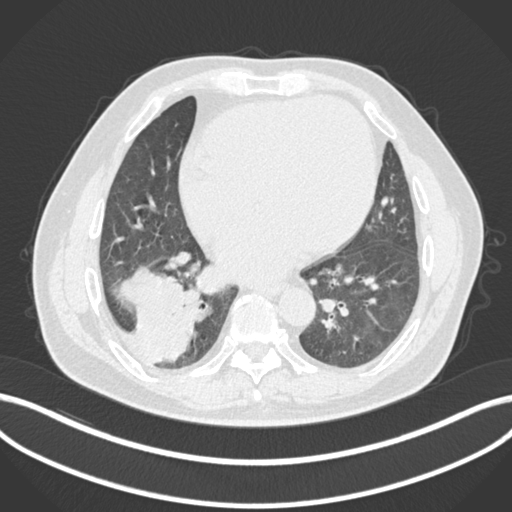
Chest CT, one axial slice. Slice 58 of 200 in the series (ordered by position). Lung window (W 1500 / L -600 HU). 512 × 512 image matrix, field of view 400 × 400 mm. Patient: male, 59 years.
Annotated regions visible in this slice (rectangle marked by the reading radiologist):
- lung tumour (recorded histology: adenocarcinoma): bounding box [x1, y1, x2, y2] px = [119, 263, 198, 366]